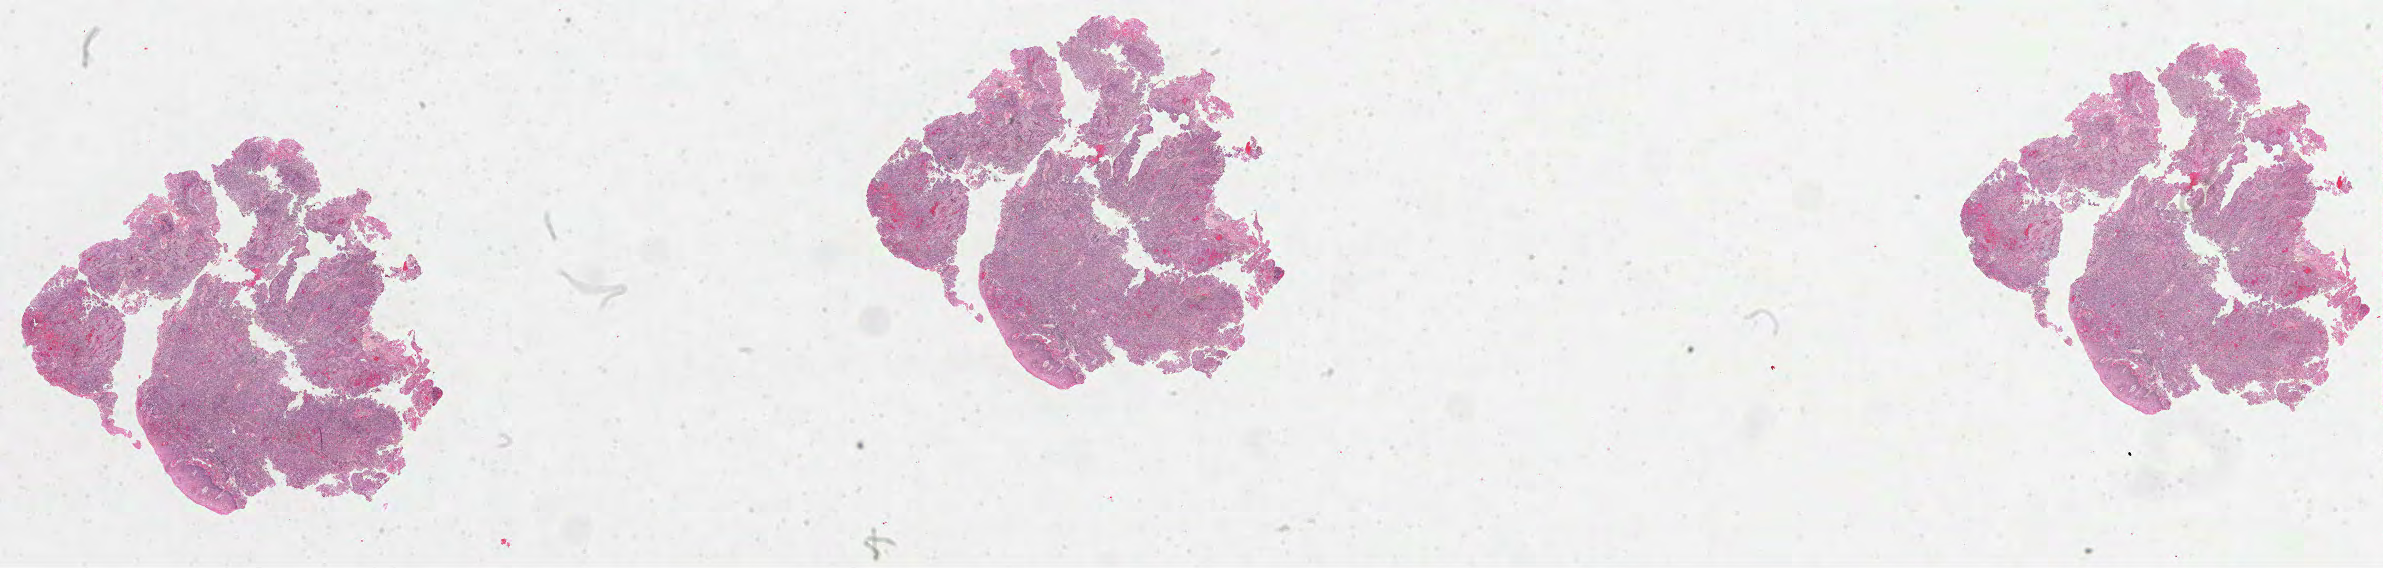
Hematoxylin and eosin (H&E) stained whole-slide image, a low-resolution overview of the entire scanned area, about 38.4 x 9.2 mm (acquisition: 40x scan); formalin-fixed paraffin-embedded (FFPE) diagnostic section; primary tumour sample from the head and neck. Male, age 39 years at initial diagnosis. Histologic grade: G2 (moderately differentiated).
• diagnosis: Squamous cell carcinoma, NOS